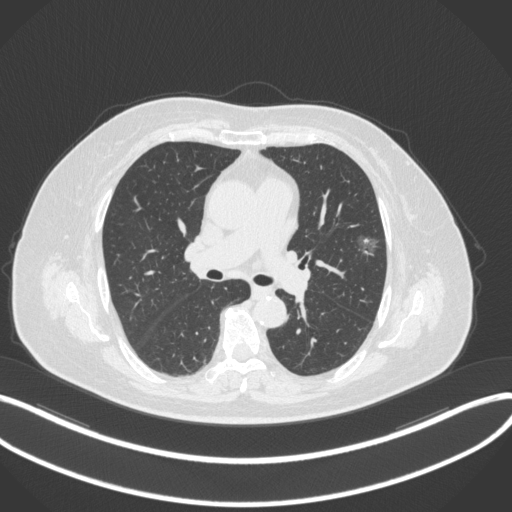
Chest CT, one axial slice; position 183 of 286 along the scan axis; 120 kVp; lung window (W 1500 / L -600 HU); 1 mm slice thickness; 512 × 512 image matrix, field of view 400 × 400 mm. Patient: female, 76 years. From the clinical record (not read from this slice): clinical TNM (as recorded): T1b N0 M0.
Annotated regions visible in this slice (rectangle marked by the reading radiologist):
- lung tumour (recorded histology: adenocarcinoma): bounding box (x1, y1, x2, y2) in pixels: (349, 225, 386, 261)